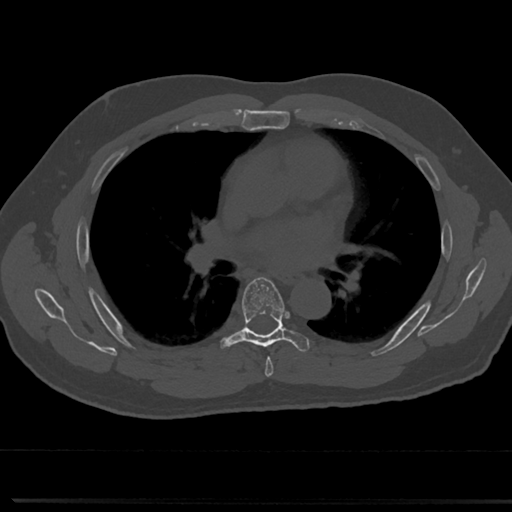
CT including the spine, one axial slice; position 458 of 817 along the scan axis; bone window (W 1800 / L 400 HU); 0.5 mm slice thickness; 512 × 512 image matrix, field of view 355 × 355 mm. Male patient, age 61 years. From the clinical record (not read from this slice): primary cancer: prostate.
Outlined on this slice (semi-automatically segmented with operator editing):
- T5 vertebra: box from (x=257, y=342) to (x=273, y=369) px
- T6 vertebra: (x=217, y=276)–(x=309, y=356)